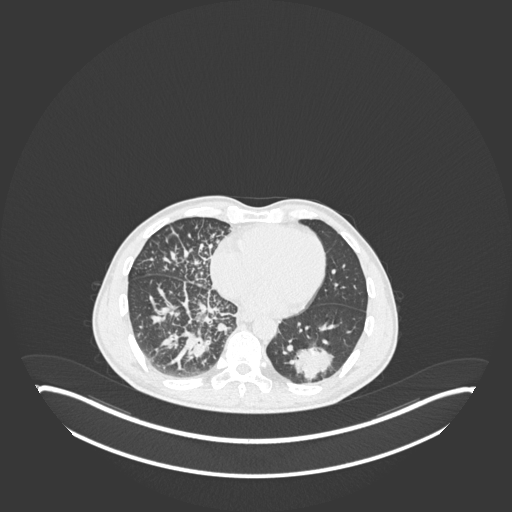
Chest CT, one axial slice. Slice 80 of 237 in the series (ordered by position). Reconstruction kernel B30f. 120 kVp. Lung window (W 1500 / L -600 HU). 1 mm slice thickness. 512 × 512 image matrix, field of view 500 × 500 mm. Male patient, age 49 years. Case-level facts recorded for this patient, not image findings: clinical TNM (as recorded): T2b N1 M0.
Structures marked on this image (bounding box drawn by a radiologist):
- lung tumour (recorded histology: adenocarcinoma): bounding box (x1, y1, x2, y2) in pixels: (286, 343, 339, 383)